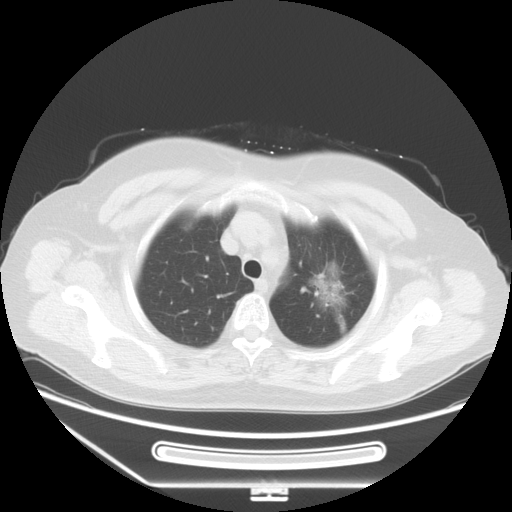
Chest CT, one axial slice. Slice 45 of 53 in the series (ordered by position). 120 kVp. Lung window (W 1500 / L -600 HU). 512 × 512 image matrix, field of view 403 × 403 mm. Patient: female, 66 years. From the clinical record (not read from this slice): clinical TNM (as recorded): T2 N0 M0.
Annotated regions visible in this slice (bounding box drawn by a radiologist):
- lung tumour (recorded histology: adenocarcinoma): bounding box (x1, y1, x2, y2) in pixels: (298, 249, 357, 330)